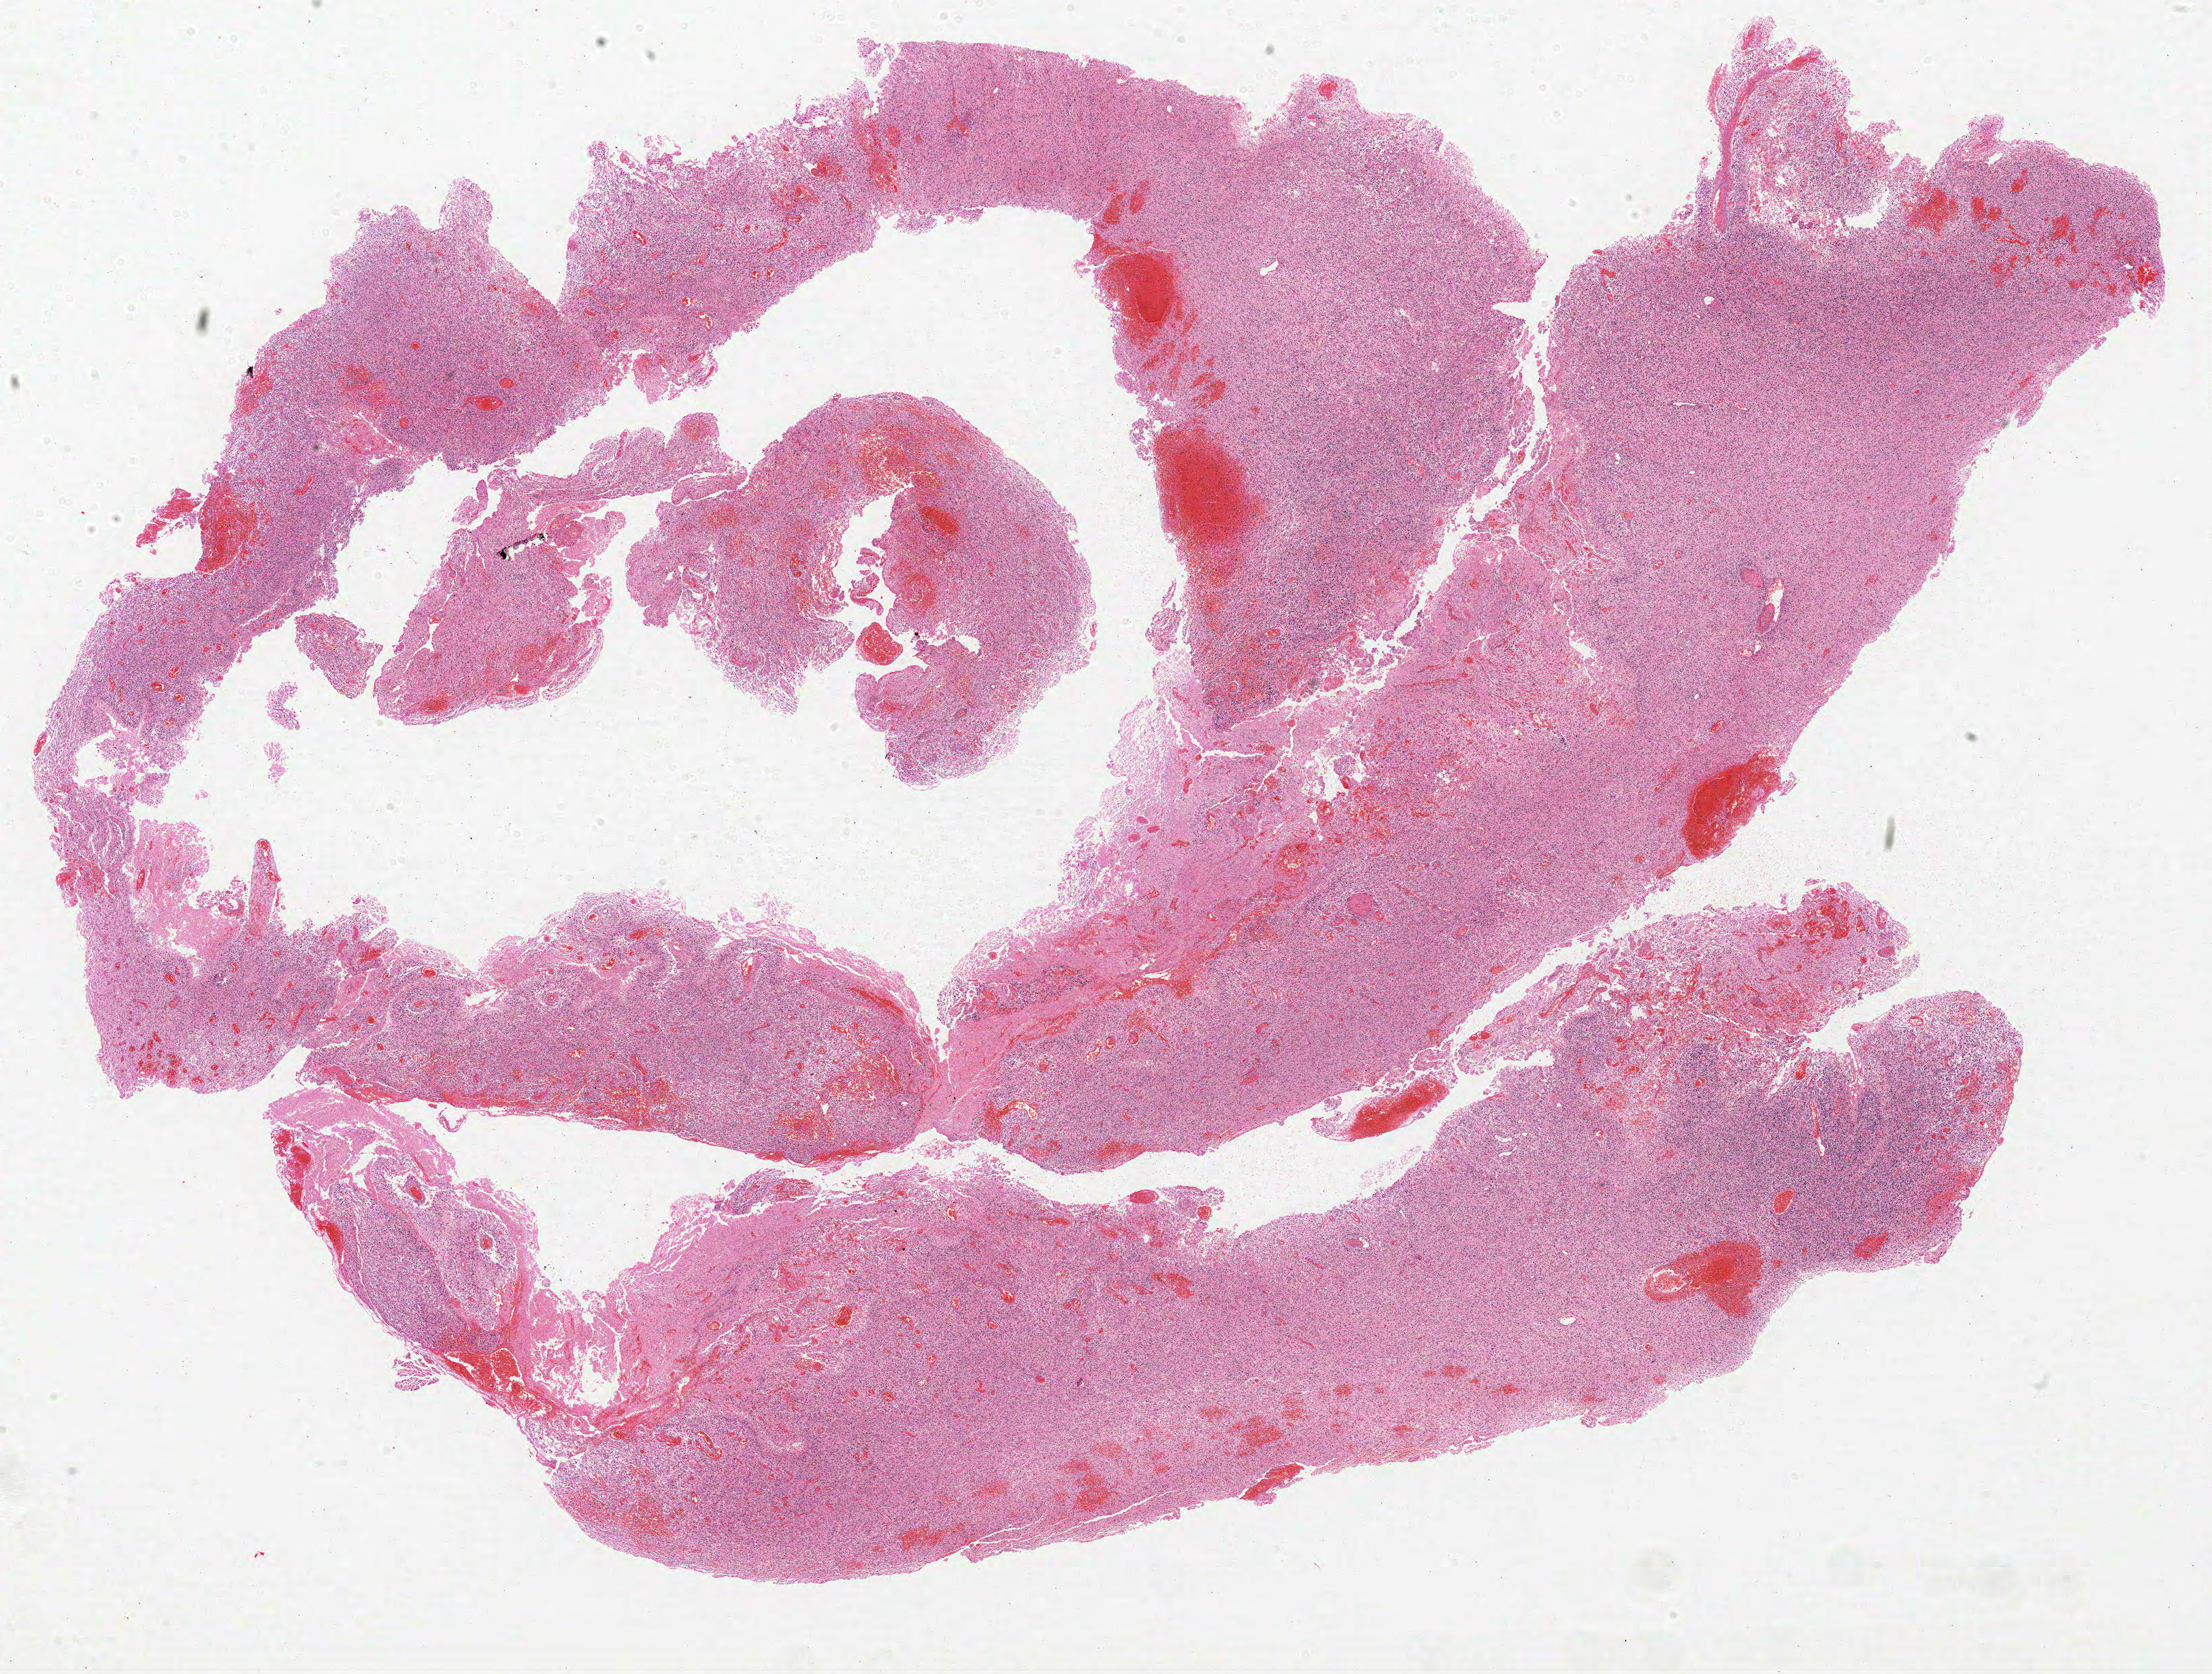
Hematoxylin and eosin (H&E) stained whole-slide image — a low-resolution overview of the entire scanned area, about 26.0 x 19.7 mm (acquisition: 20x scan). FFPE section. Primary tumour sample from the brain. Female patient; age at initial diagnosis 53 years.
• histologic diagnosis: Glioblastoma